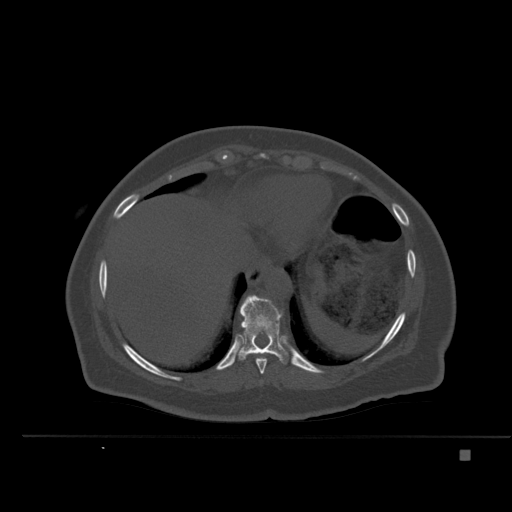
CT including the spine, one axial slice. Slice 287 of 477 in the series (ordered by position). Bone window (W 1800 / L 400 HU). 1.5 mm slice thickness. 512 × 512 image matrix, field of view 422 × 422 mm. Patient: female, 74 years. Case-level facts recorded for this patient, not image findings: primary cancer: colon.
Structures marked on this image (semi-automatically segmented with operator editing):
- T10 vertebra: box from (x=239, y=295) to (x=288, y=364) px
- T9 vertebra: (x=247, y=352)–(x=271, y=374)